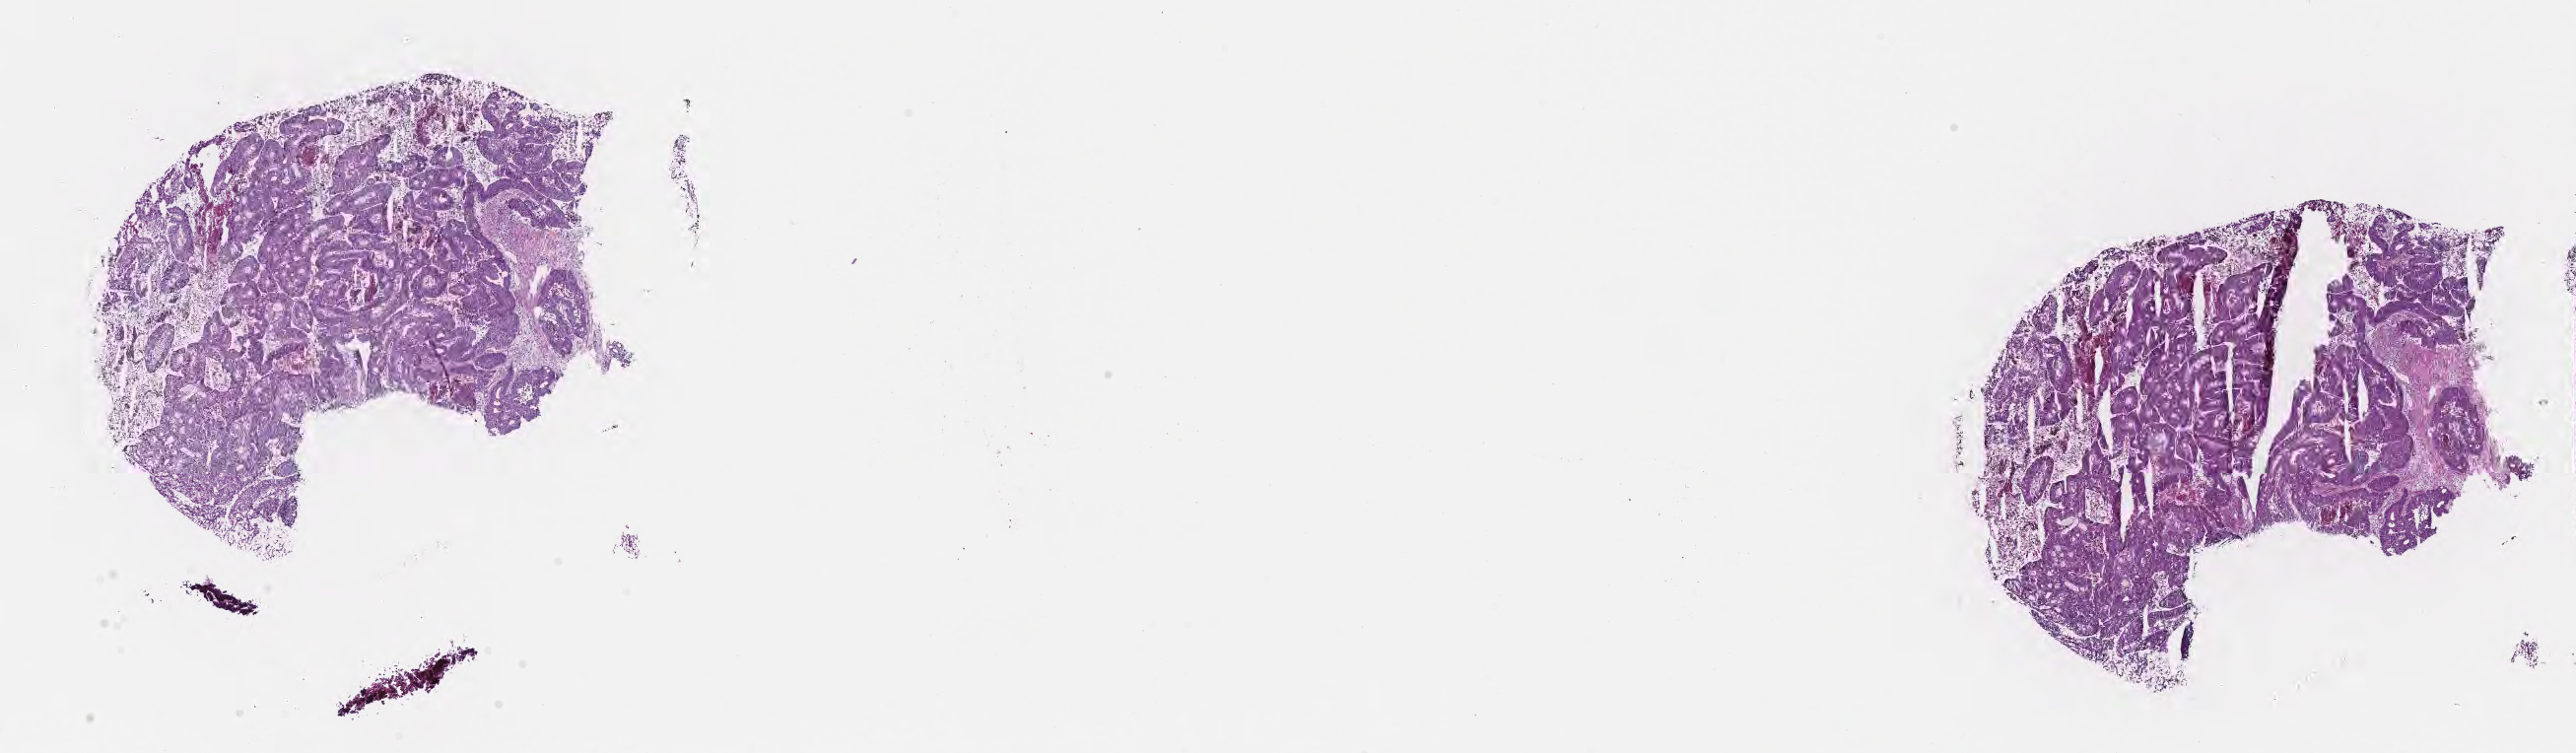
Digitized hematoxylin and eosin (H&E)-stained section, a low-resolution overview of the entire scanned area, about 21.1 x 6.2 mm, frozen section (tissue freezing medium), primary tumor. Female, age 76 years at initial diagnosis. Tumor grade: G2 (moderately differentiated). Slide review estimates, as recorded: tumor cells 85%, tumor nuclei 85%, stromal cells 14%, necrosis 1%, normal cells 0%. Infiltration values recorded for this section: lymphocyte infiltration 3%, monocyte infiltration 1%, neutrophil infiltration 5%.
AJCC pathologic stage: Stage IVA. Diagnosis: Adenocarcinoma, metastatic, NOS. Section: top of the tissue portion.